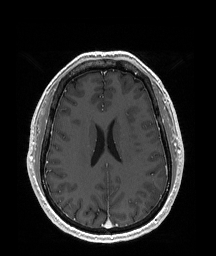
Brain MRI from a brain-tumour surgery series, one axial slice. Position 80 of 192 along the scan axis. T1-weighted post-contrast. 1 mm slice thickness. 216 × 256 image matrix, field of view 219 × 260 mm. Case-level facts recorded for this patient, not image findings: histopathology: Glioblastoma; WHO grade: 4; IDH mutation: no.
Structures marked on this image (expert manual segmentation):
- tumour: bounding box <142,181,164,207> (left, top, right, bottom; pixels)